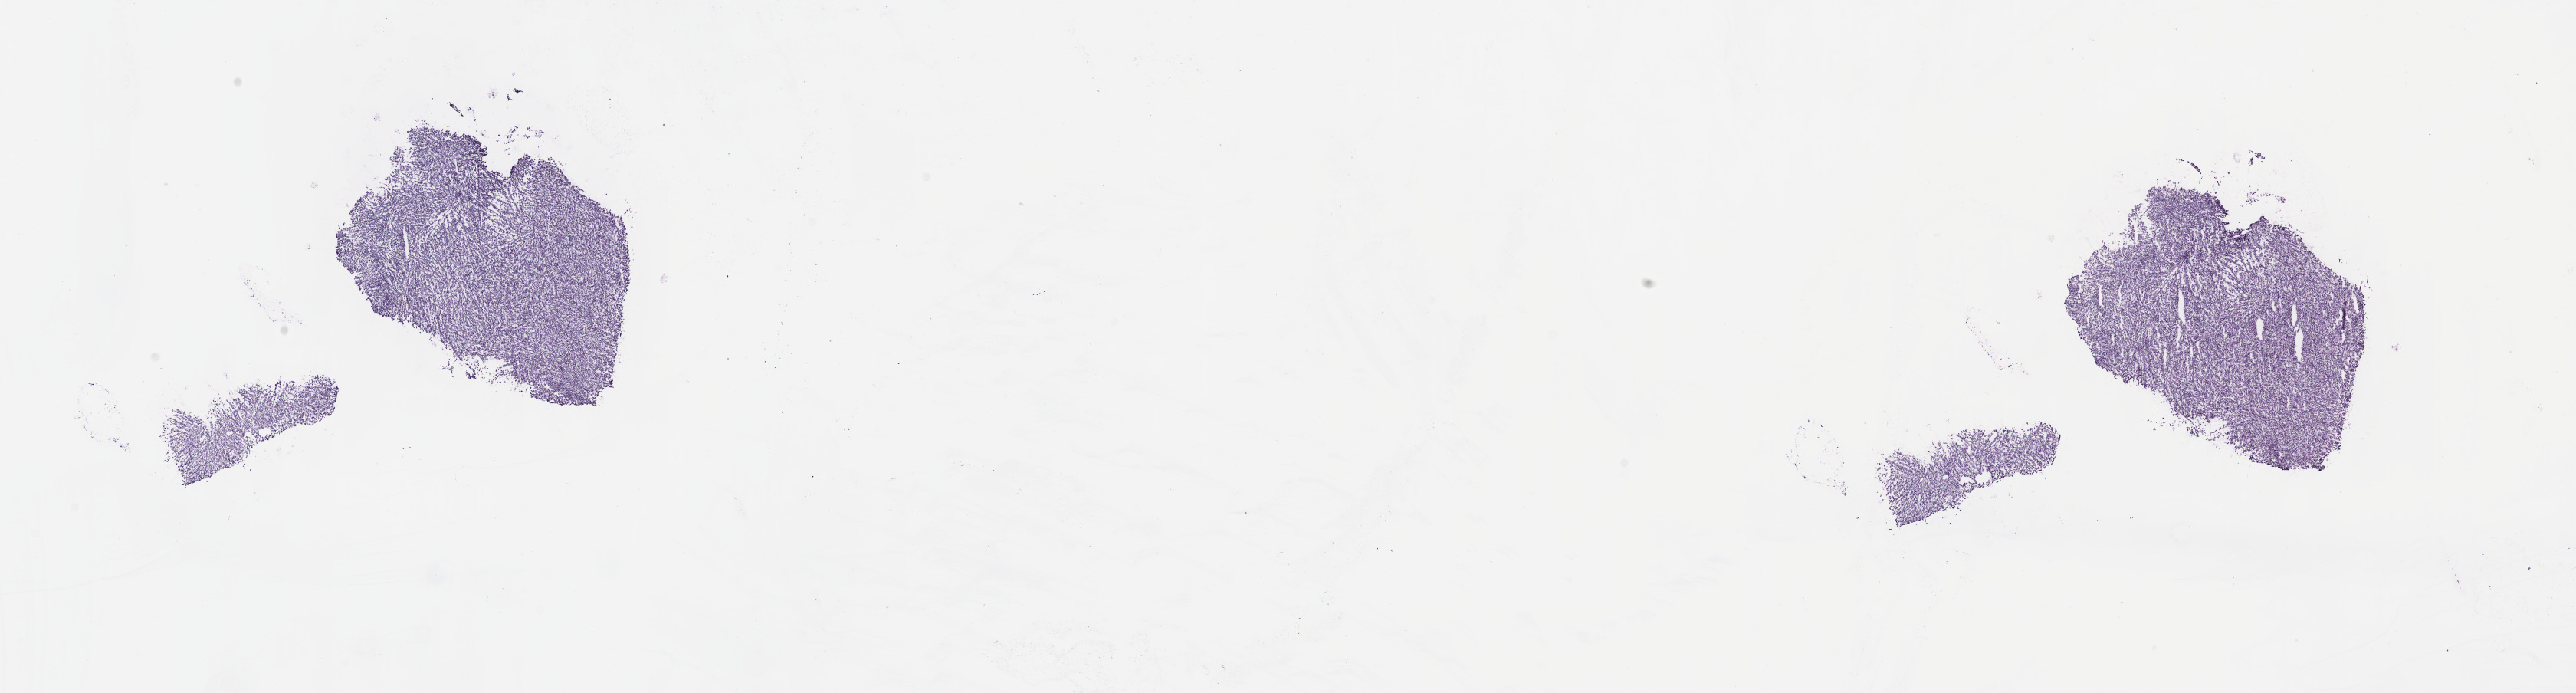
Digitized Hematoxylin and eosin (H&E) stained tissue section (whole slide) — a low-resolution overview of the entire scanned area, about 27.2 x 7.3 mm. Frozen section from the top of the tissue portion. Uvea, primary tumour sample. Male, age 63 years at initial diagnosis. Composition of this section per pathologist review: tumour cells 80%, tumour nuclei 80%.
Pathologic diagnosis: Mixed epithelioid and spindle cell melanoma.